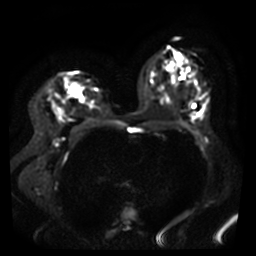
Breast MRI, one axial slice. Position 24 of 46 along the scan axis. Diffusion-weighted series; image 2 of 4 stored at this slice position (different b-values; order by instance number). 3 T. 5 mm slice thickness. 256 × 256 image matrix, field of view 360 × 360 mm. Female patient.
Annotated regions visible in this slice (outlined manually by an expert reader):
- tumour on diffusion-weighted imaging: box from (x=54, y=106) to (x=62, y=118) px